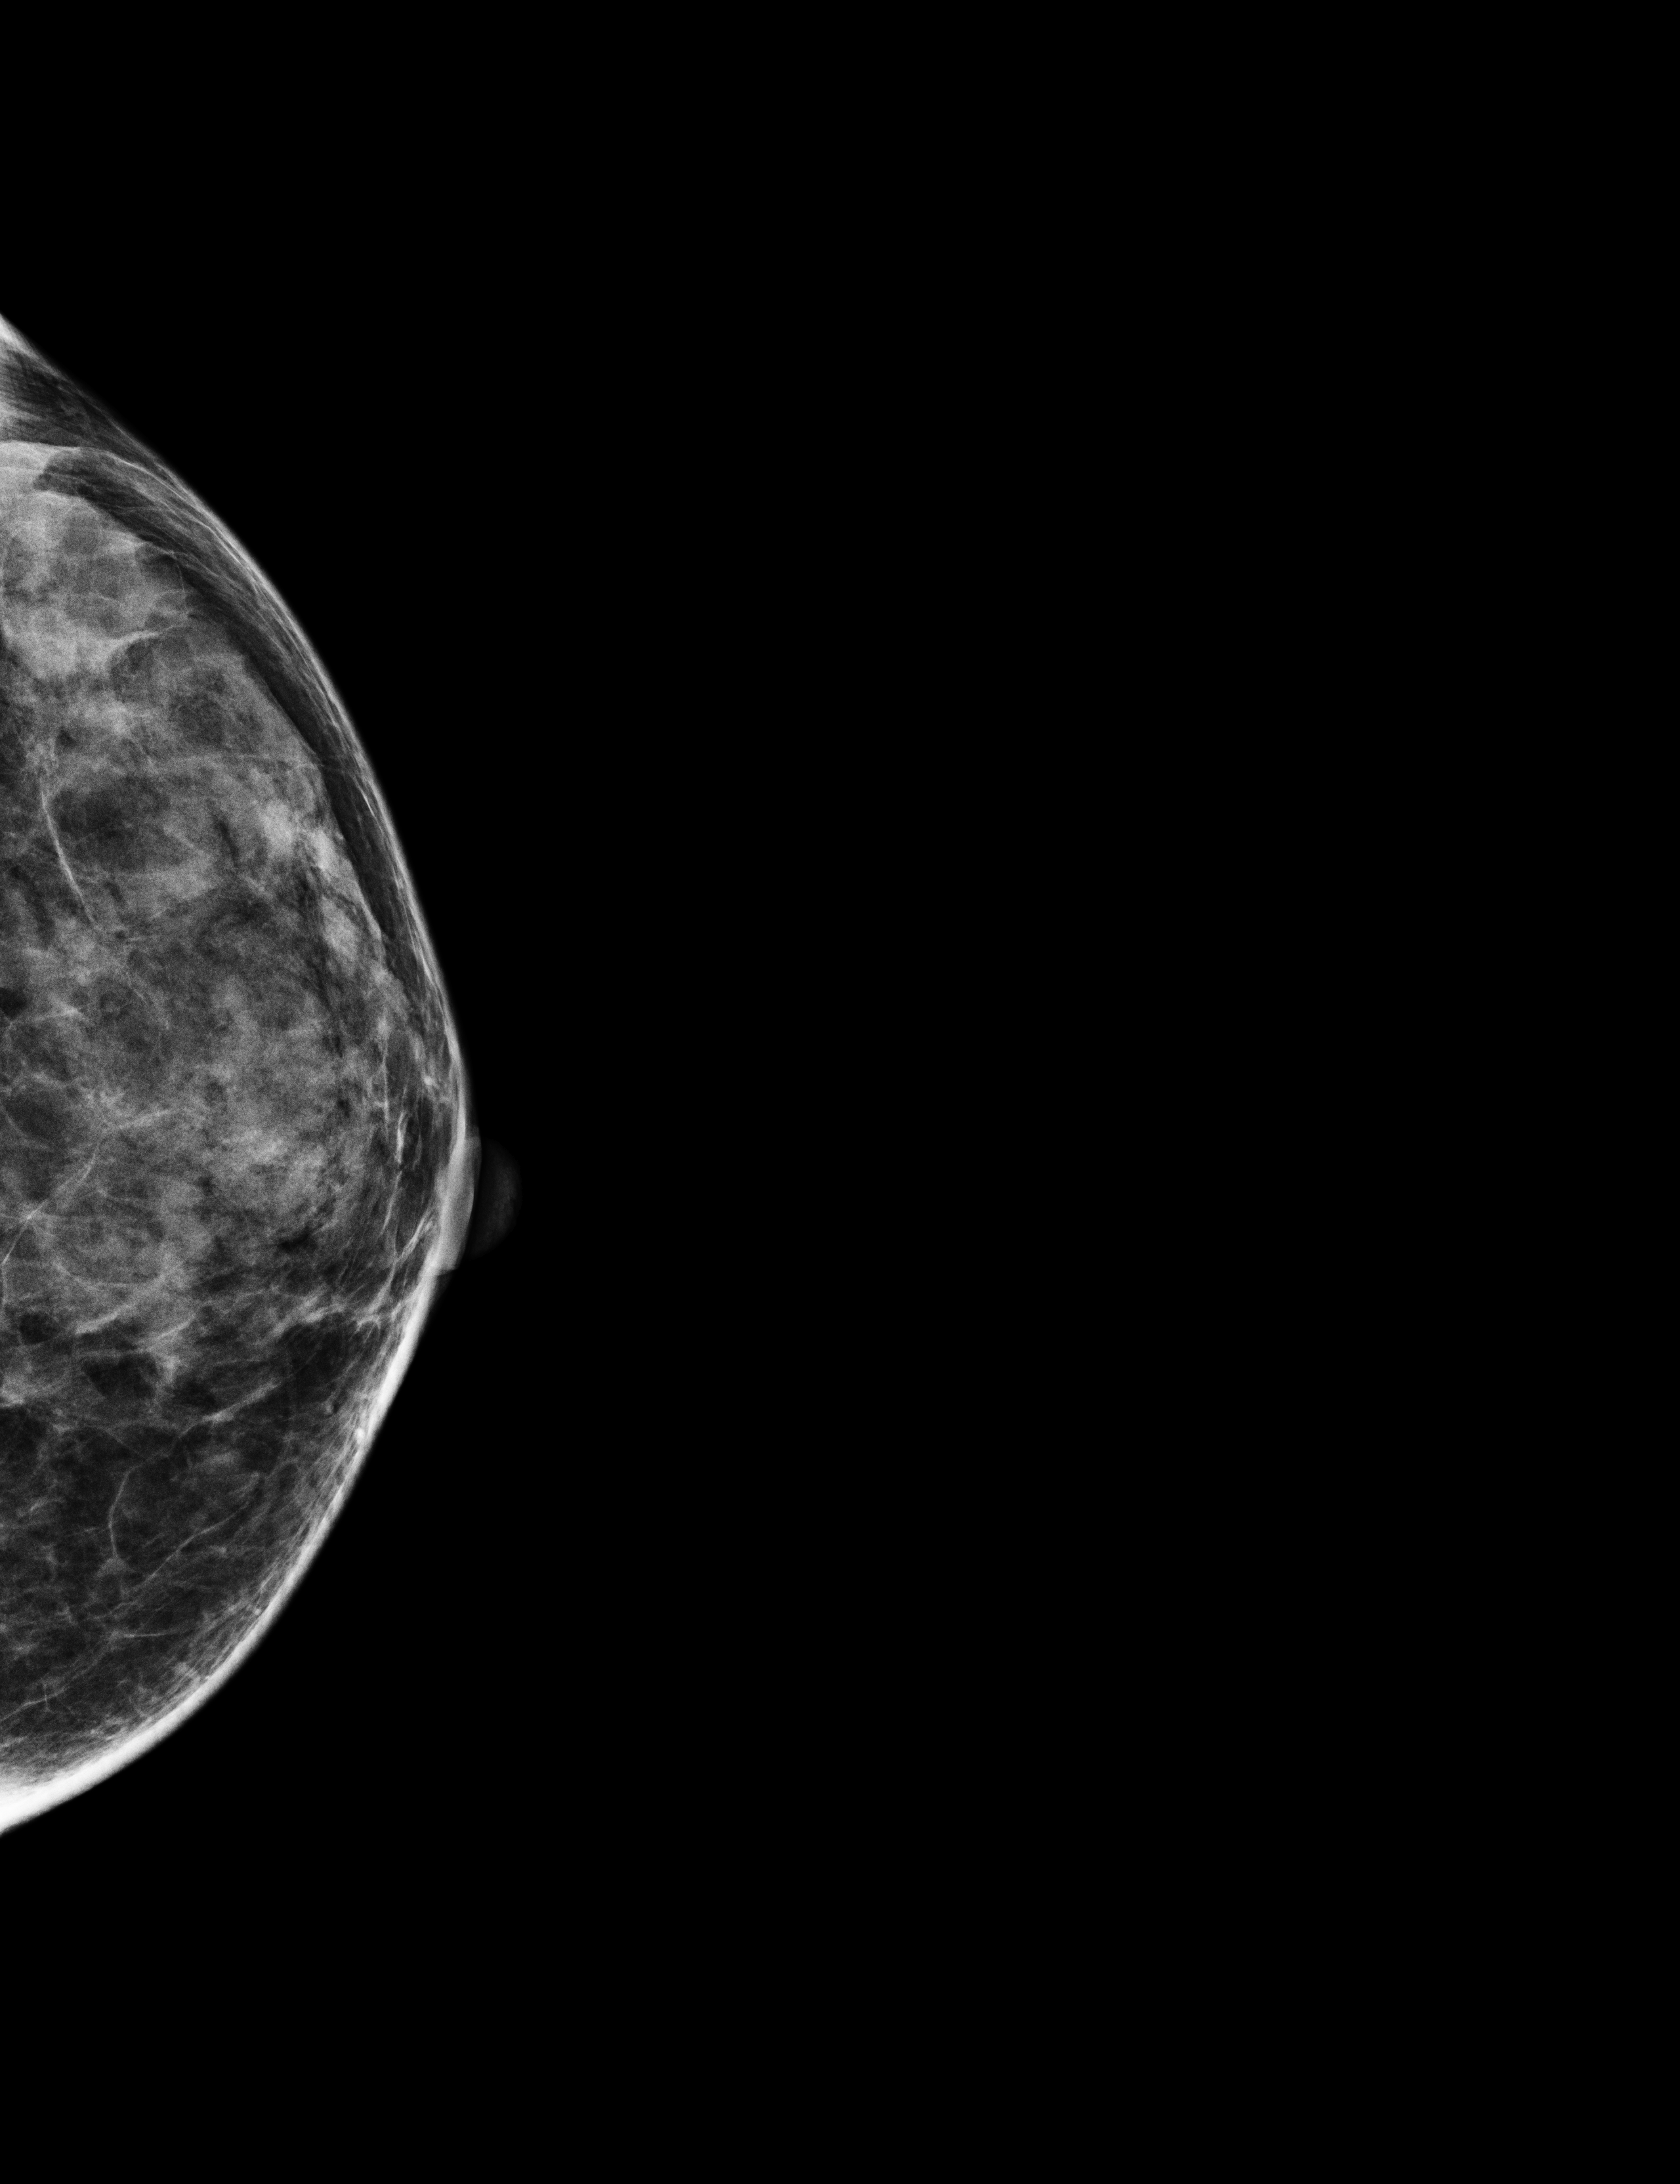
Screening examination; compressed breast thickness 35 mm. Patient aged 43 years (female).
Image type: full-field digital mammogram. Breast: left. Projection: craniocaudal (CC) view.